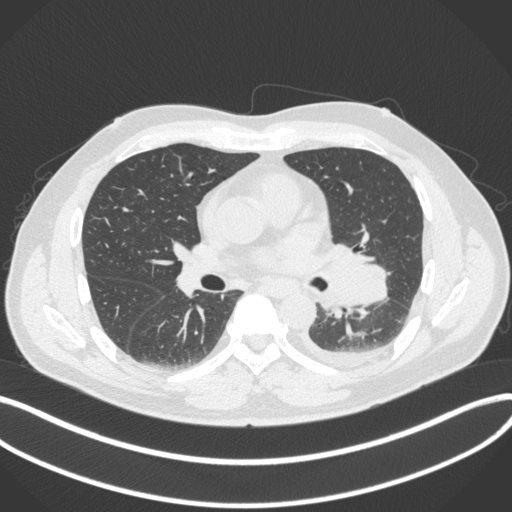
Chest CT, one axial slice; position 192 of 350 along the scan axis; reconstruction kernel B31f; 120 kVp; lung window (W 1500 / L -600 HU); 1 mm slice thickness; 512 × 512 image matrix, field of view 400 × 400 mm. Patient: male, 58 years. From the clinical record (not read from this slice): clinical TNM (as recorded): T3 N1 M1b; histopathological grade: G3.
Structures marked on this image (rectangle marked by the reading radiologist):
- lung tumour (recorded histology: small cell carcinoma): bounding box (x1, y1, x2, y2) in pixels: (315, 239, 393, 324)